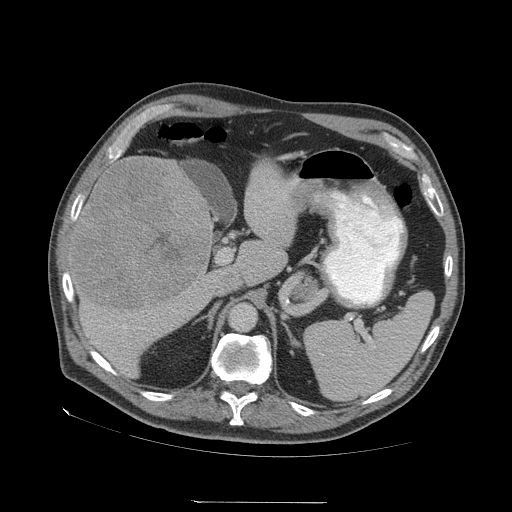
Contrast-enhanced abdominal CT (liver protocol), one axial slice. Position 33 of 83 along the scan axis. Reconstruction kernel STANDARD. Soft-tissue window (W 400 / L 40 HU). 512 × 512 image matrix. Case-level facts recorded for this patient, not image findings: diagnosis: hepatocellular carcinoma (patient treated with transarterial chemoembolisation; whether this scan precedes or follows treatment is not stated here); TNM stage (as recorded): Stage-I; Child-Pugh class: A; tumour nodularity: uninodular.
Annotated regions visible in this slice (semi-automatic segmentation, software-assisted and operator-edited):
- liver parenchyma outside the tumour (the mass and vessels are separate outlines, so this box may not span the whole liver): bounding box [x1, y1, x2, y2] px = [68, 156, 296, 378]
- mass: [72, 156, 211, 309]
- liver vessels: [124, 326, 126, 328]